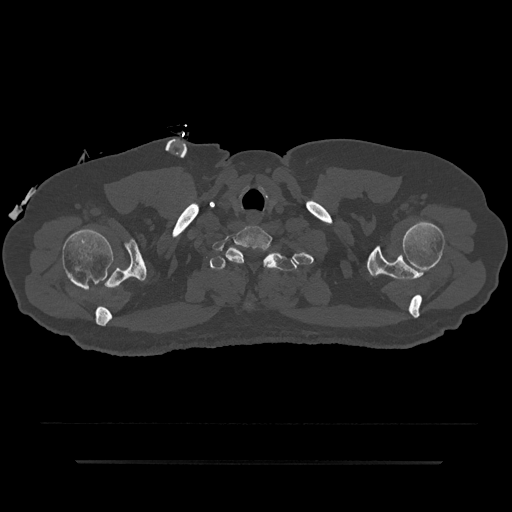
CT including the spine, one axial slice; 120 kVp; bone window (W 1800 / L 400 HU); 0.5 mm slice thickness; 512 × 512 image matrix. Male patient, age 59 years. Case-level facts recorded for this patient, not image findings: primary cancer: bile ducts.
Annotated regions visible in this slice (semi-automatically segmented with operator editing):
- T1 vertebra: bounding box (x1, y1, x2, y2) in pixels: (210, 249, 298, 307)